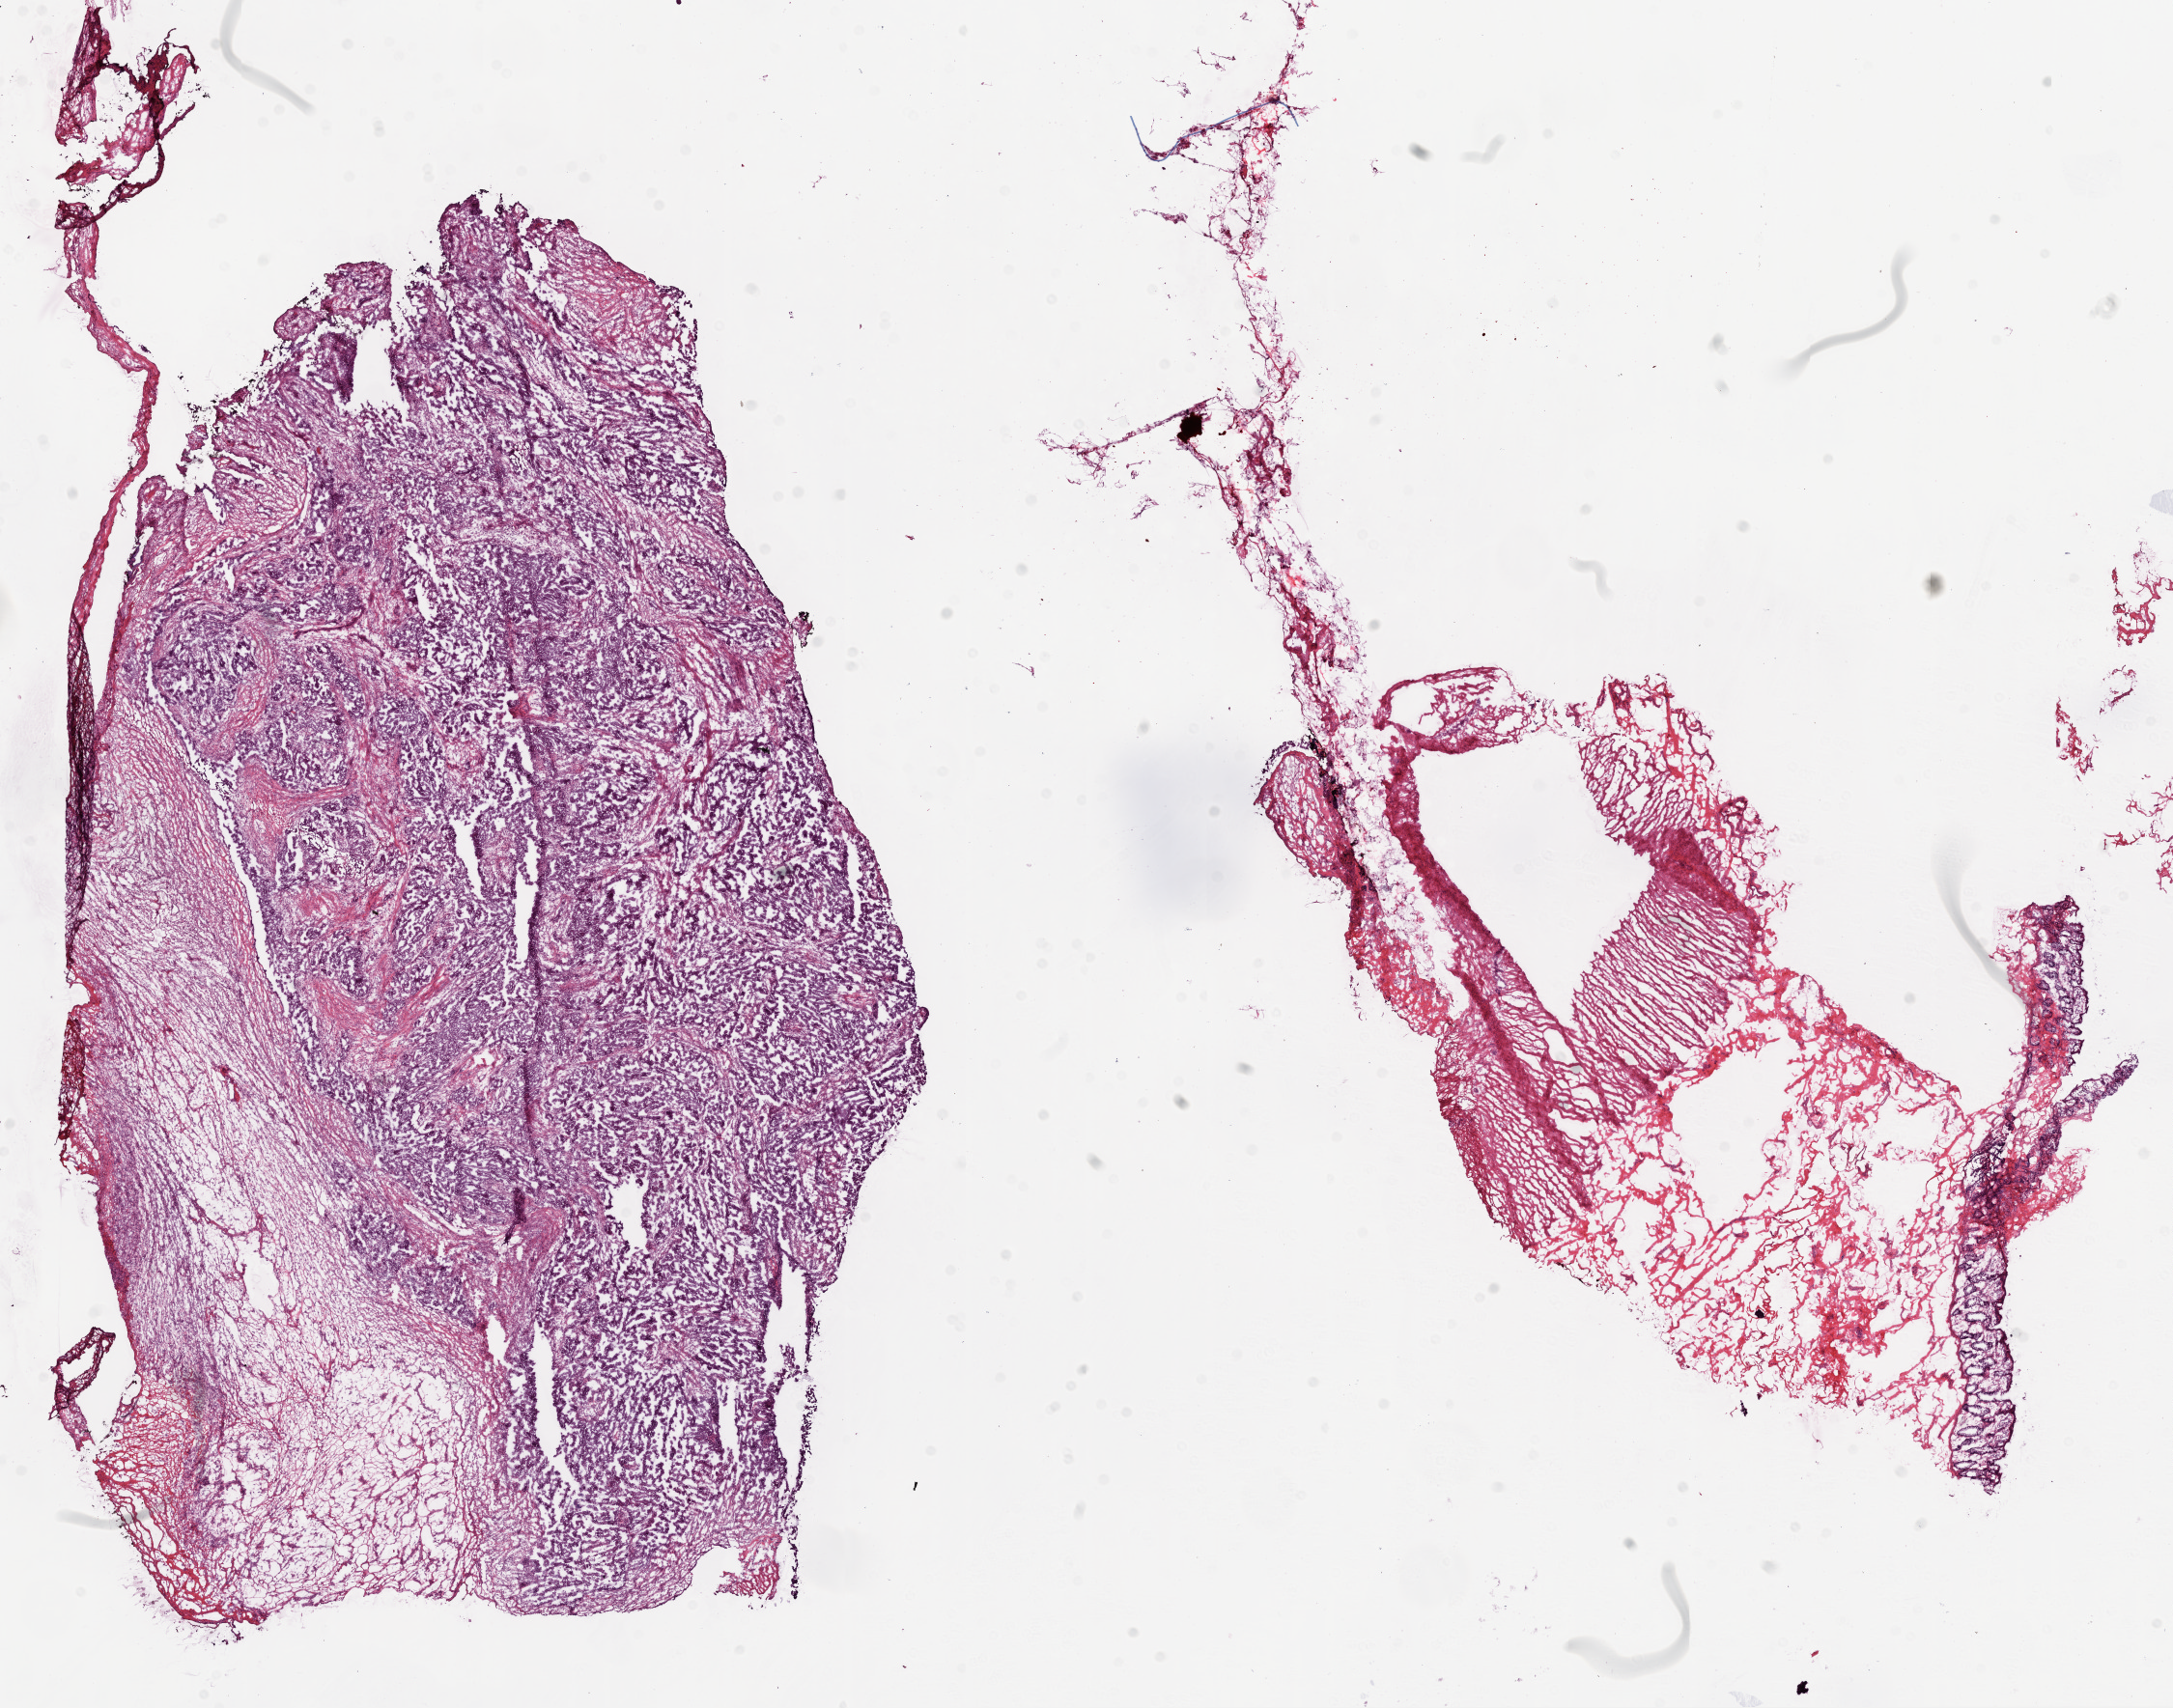
Hematoxylin and eosin (H&E) stained whole-slide image — a low-resolution overview of the entire scanned area, about 18.1 x 14.2 mm. Frozen section from the bottom of the tissue portion. Sample: primary tumour, ovary. Female, age 43 years at initial diagnosis. Histologic grade: G3 (poorly differentiated). Pathologist review of this section (percent, as recorded): tumour cells 90%, tumour nuclei 90%, normal cells 0%, stromal cells 10%, necrosis 0%.
Diagnosis: Serous cystadenocarcinoma, NOS. FIGO stage: IV. Laterality: bilateral.